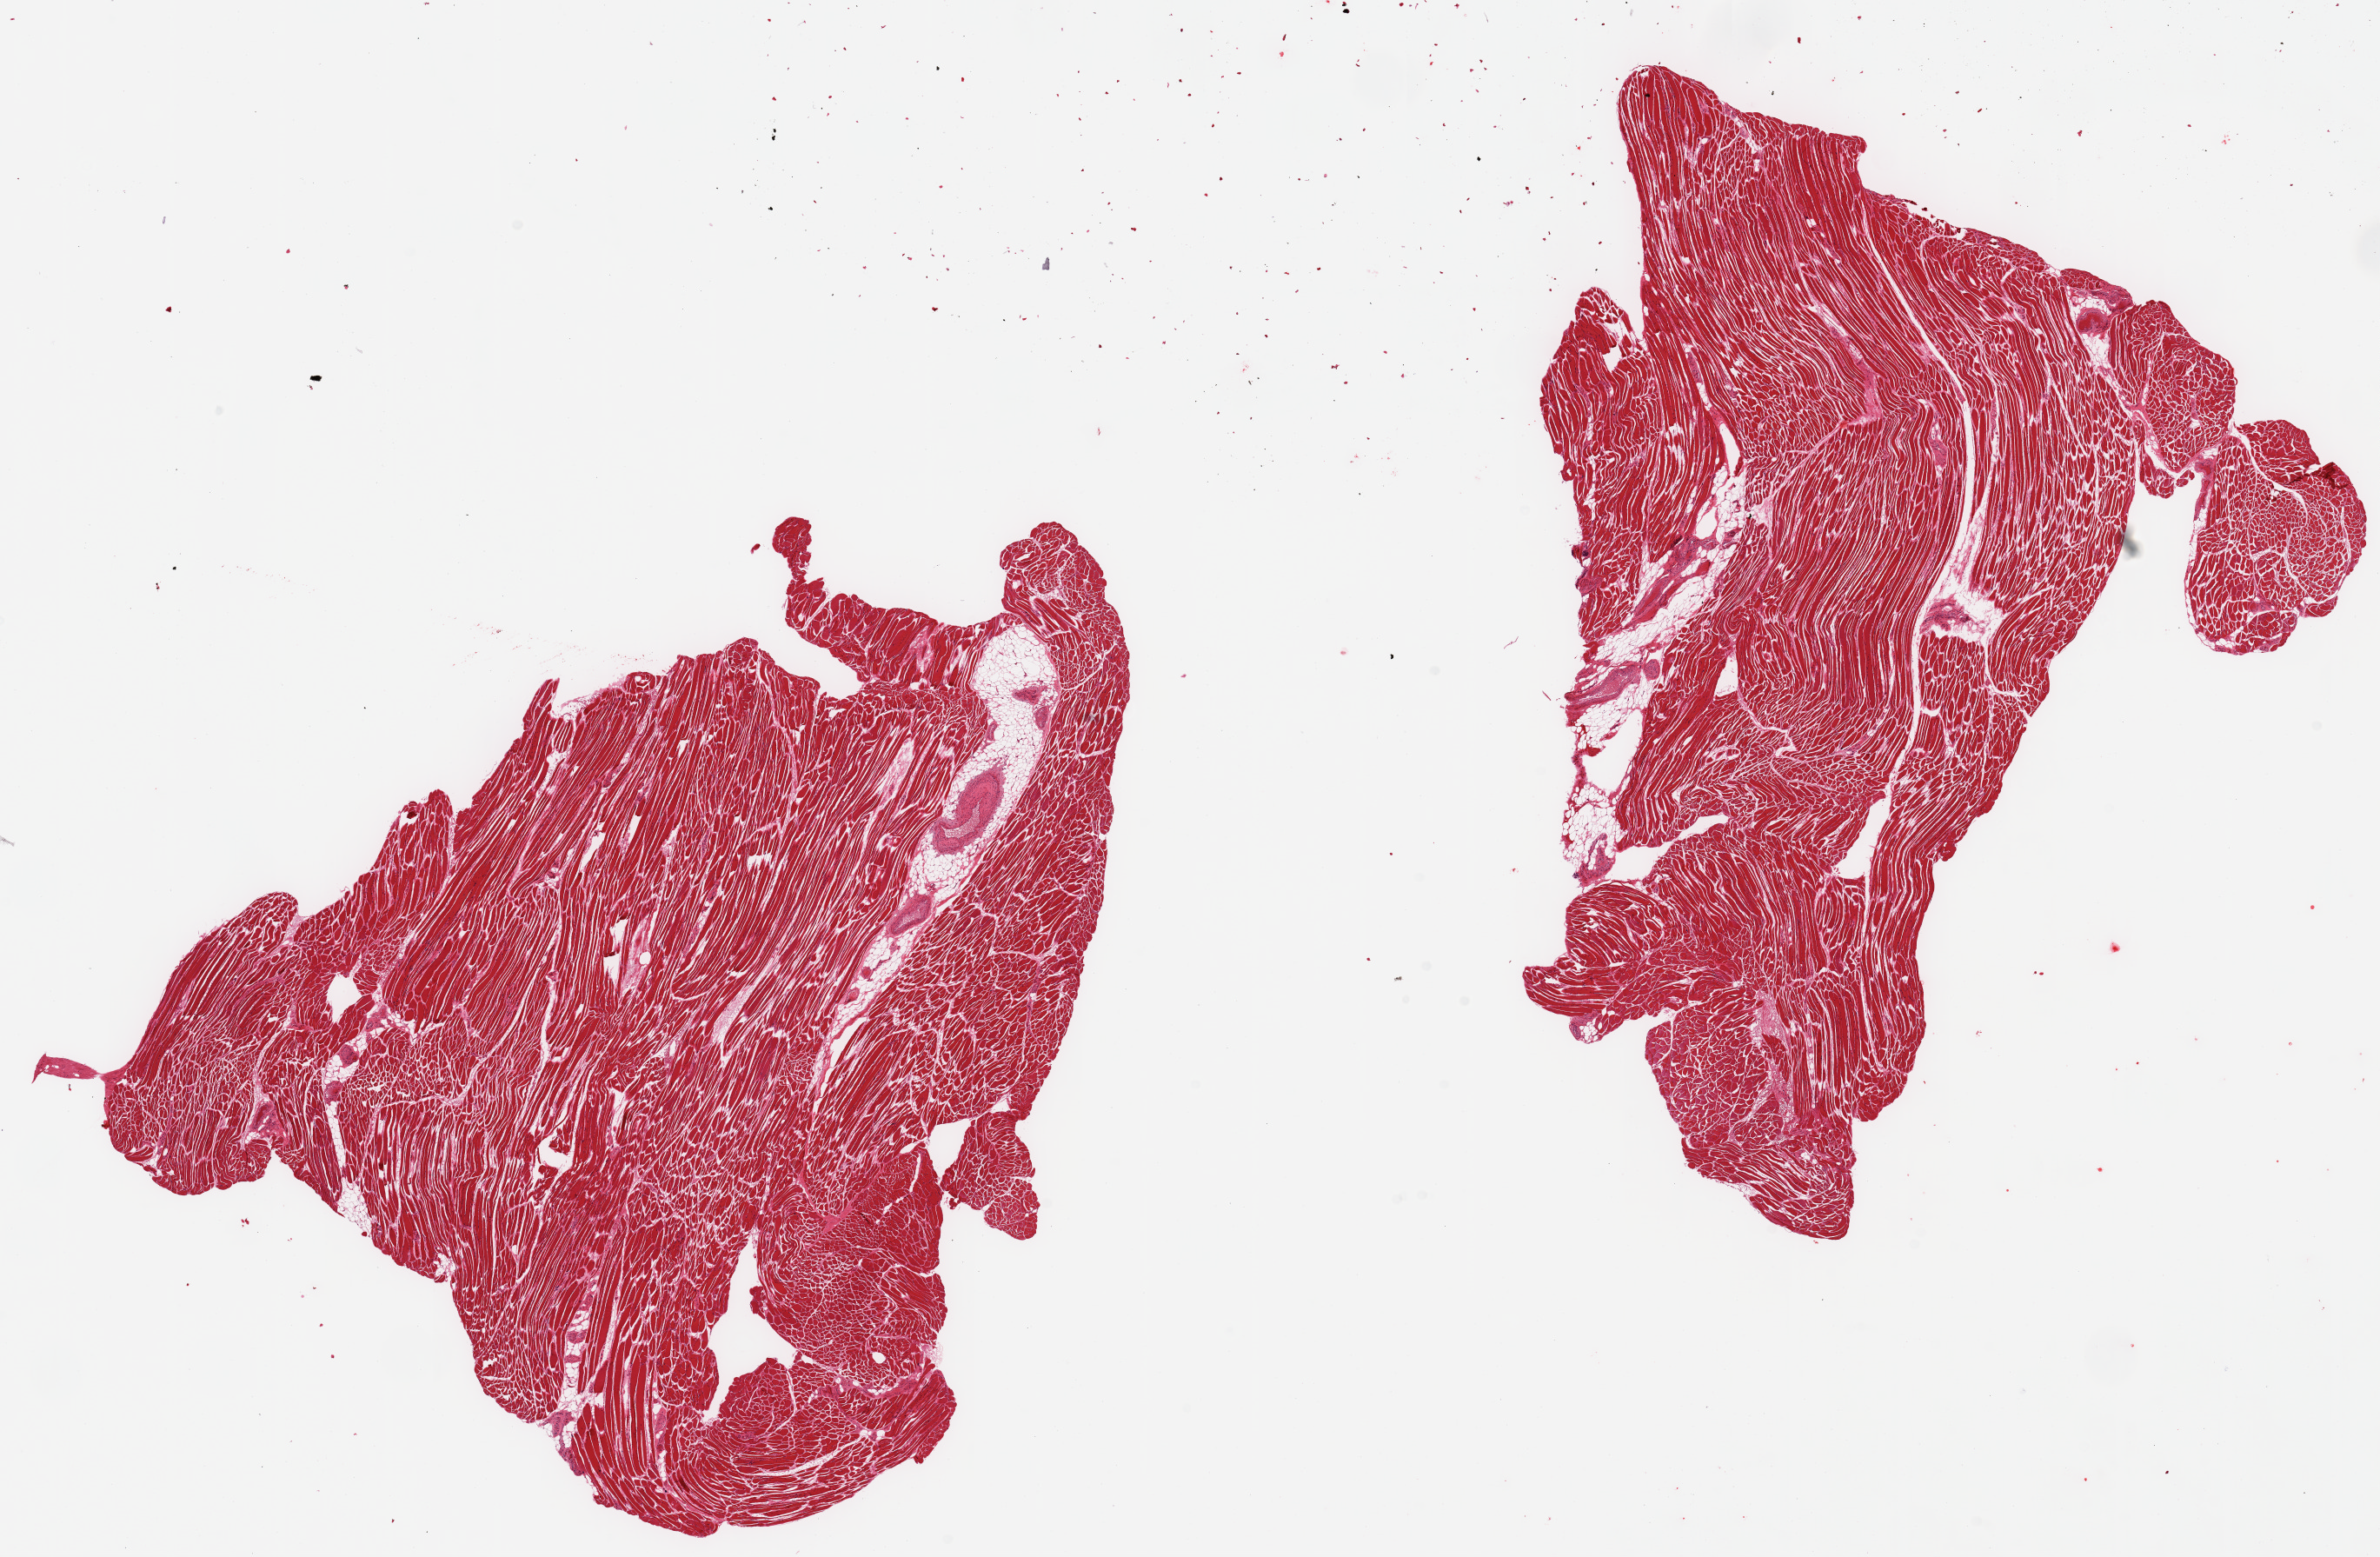
H&E whole-slide image — a low-resolution overview of the entire scanned area, about 21.7 x 14.2 mm (slide scanned at 20x), PAXgene-fixed paraffin-embedded (PFPE) section, sampled site (target tissue): skeletal muscle, tissue donor sample.
Reviewer comment on this tissue sample: 2 pieces; well trimmed.